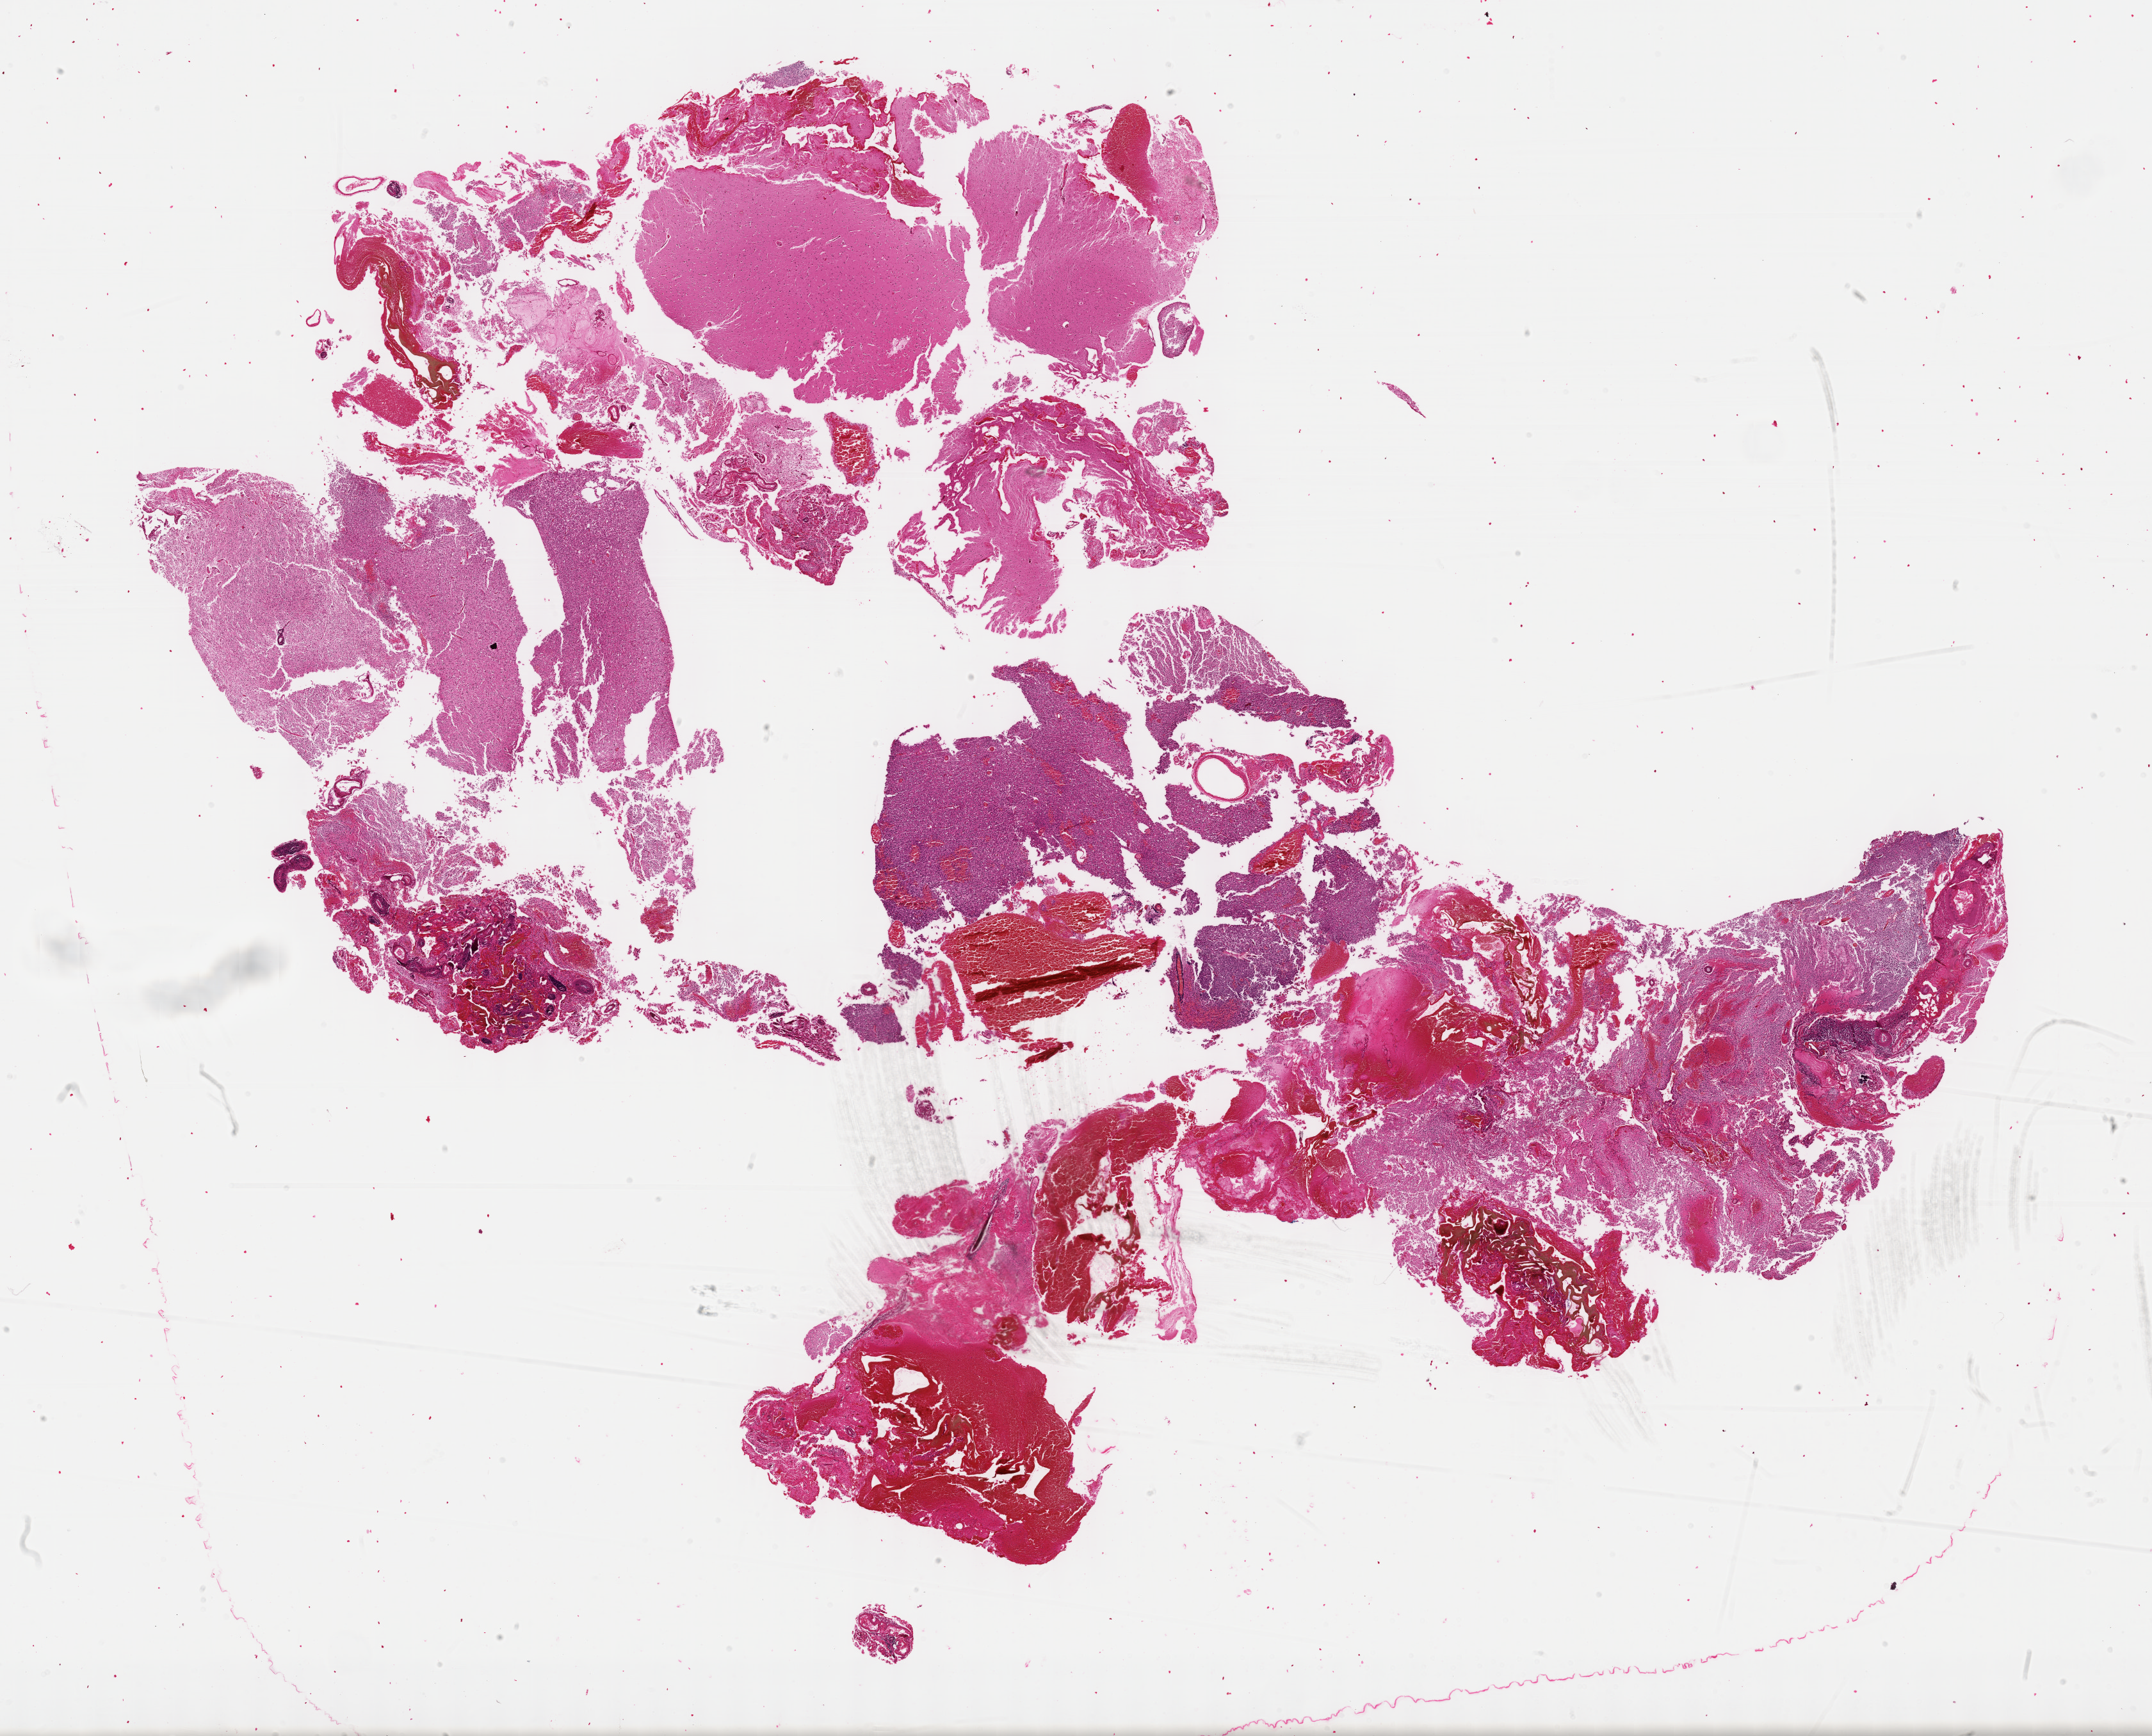
H&E-stained whole-slide image, whole scanned area (about 27.2 x 21.9 mm, slide scanned at 40x) shown as a low-resolution overview, FFPE section, sample: primary tumour, brain. Patient: male, age at initial diagnosis 46 years. Histologic grade: G2 (moderately differentiated).
- histologic diagnosis: Oligodendroglioma, NOS (cerebrum)